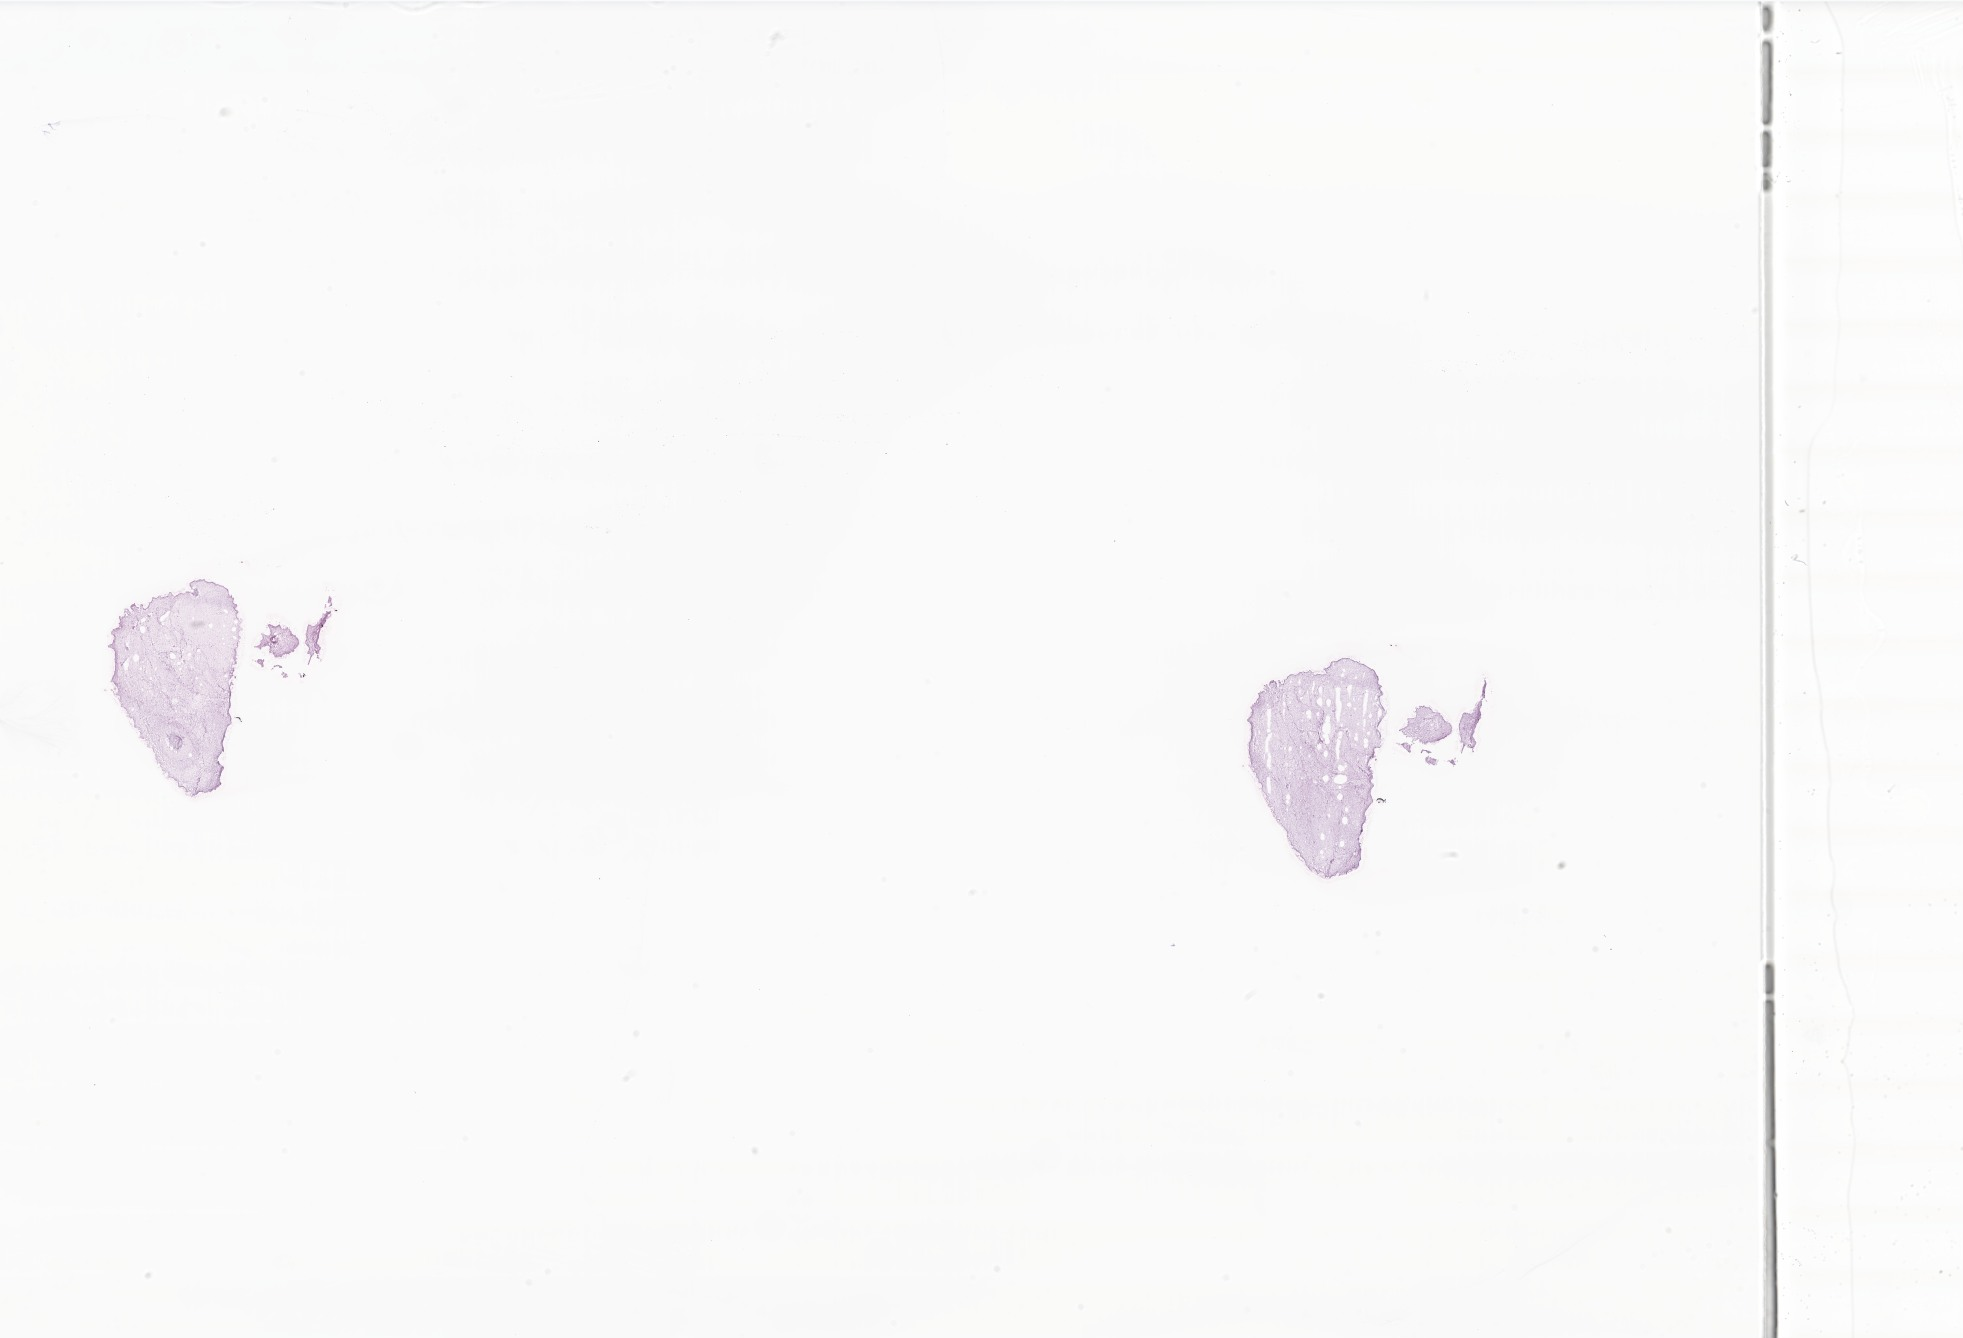
Haematoxylin and eosin whole-slide image of tumor tissue from the brain — a low-resolution overview of the entire scanned area, about 33.1 x 22.6 mm; cryosection (OCT / tissue freezing medium). Patient: female, age 168 months (14 years).
Diagnosis (ICD-O-3 morphology term): Pilocytic astrocytoma.